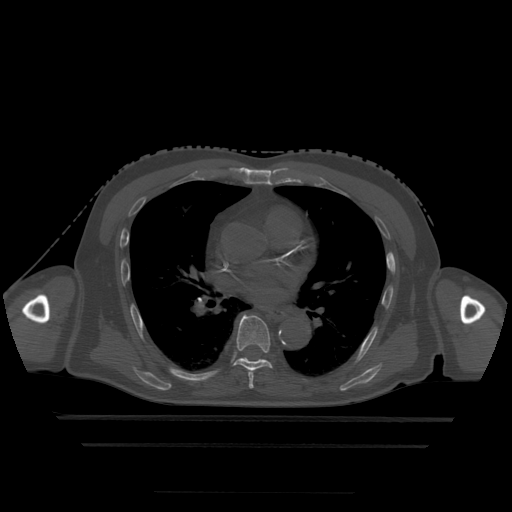
CT including the spine, one axial slice; bone window (W 1800 / L 400 HU); 1.25 mm slice thickness; 512 × 512 image matrix, field of view 436 × 436 mm. Patient age 68 years. Case-level facts recorded for this patient, not image findings: primary cancer: urothelial.
Annotated regions visible in this slice (semi-automatically segmented with operator editing):
- T6 vertebra: bounding box <248,370,254,389> (left, top, right, bottom; pixels)
- T7 vertebra: <234,314,272,373>